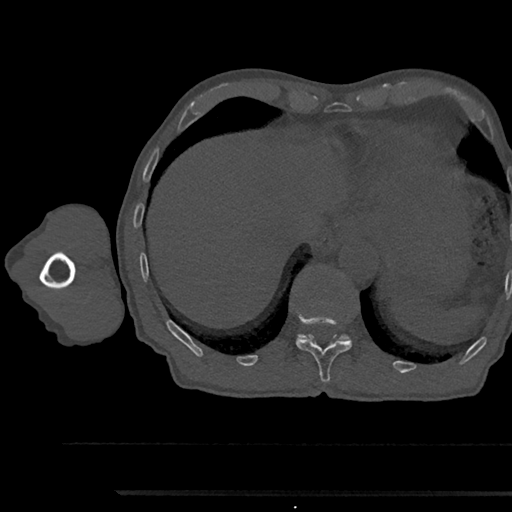
CT including the spine, one axial slice. Slice 766 of 797 in the series (ordered by position). Bone window (W 1800 / L 400 HU). 0.5 mm slice thickness. 512 × 512 image matrix, field of view 367 × 367 mm. Patient: male, 79 years. Case-level facts recorded for this patient, not image findings: primary cancer: prostate.
Outlined on this slice (semi-automatically segmented with operator editing):
- T11 vertebra: bounding box [x1, y1, x2, y2] px = [296, 318, 352, 383]
- T12 vertebra: [297, 333, 351, 341]